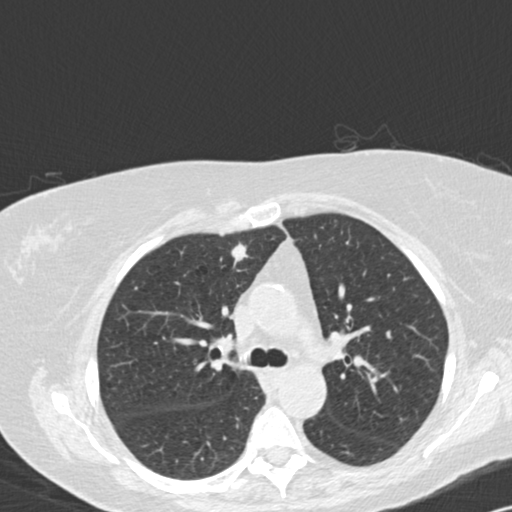
Low-dose screening chest CT, axial slice, third annual screen, lung window (W 1500 / L -600 HU), standard (soft-tissue) reconstruction kernel (B30f), 120 kVp, slice 45 of 141 in the series. Female, age 72 years at enrolment. Former smoker at enrolment.
Expert-annotated lung lesion, bounding box (x1, y1, x2, y2) in pixels: (217, 234, 263, 279). Reader record for this screening exam (exam-level; its link to the box is not recorded): non-calcified nodule or mass ≥4 mm, right upper lobe, 8 × 8 mm, spiculated (stellate) margins, soft tissue attenuation, pre-existing on the prior screen: yes; interval growth: yes. Official screen result: positive, other. Later outcome: lung cancer diagnosed 154 days after this screen — adenocarcinoma, NOS, right upper lobe, moderately differentiated (G2), stage IA (AJCC 6th edition), 15 mm at pathology.